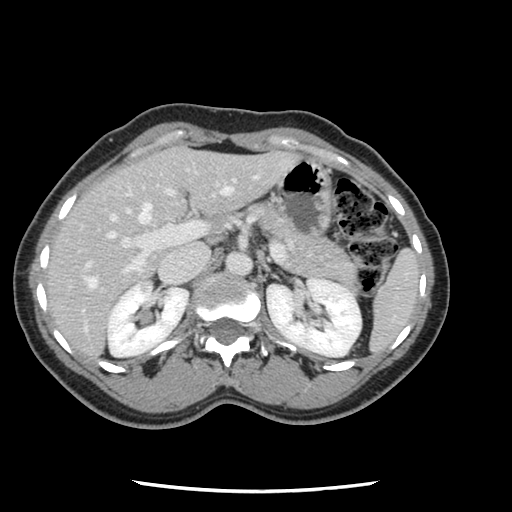
Contrast-enhanced abdominal CT, one axial slice; position 71 of 134 along the scan axis; 120 kVp; intravenous contrast given; soft-tissue window (W 400 / L 40 HU); 2.5 mm slice thickness; 512 × 512 image matrix, field of view 330 × 330 mm. Female patient, age 43 years. Case-level facts recorded for this patient, not image findings: diagnosis: colorectal cancer liver metastases, imaged before liver resection; multiple liver metastases: yes.
Outlined on this slice (manually delineated by an expert):
- hepatic veins: bounding box [x1, y1, x2, y2] px = [85, 187, 232, 330]
- liver: [47, 147, 294, 358]
- planned liver remnant (the part of the liver to remain after resection): [47, 150, 186, 303]
- portal vein (with intrahepatic branches): [69, 179, 235, 290]